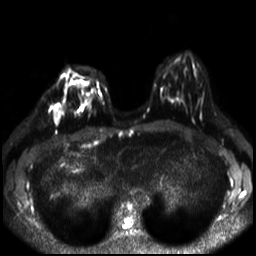
Breast MRI, one axial slice. Position 11 of 30 along the scan axis. Diffusion-weighted series; image 2 of 4 stored at this slice position (different b-values; order by instance number). 3 T. 4 mm slice thickness. 256 × 256 image matrix. Female patient.
Annotated regions visible in this slice (manually delineated by an expert):
- tumour on diffusion-weighted imaging: bounding box (x1, y1, x2, y2) in pixels: (55, 103, 59, 123)